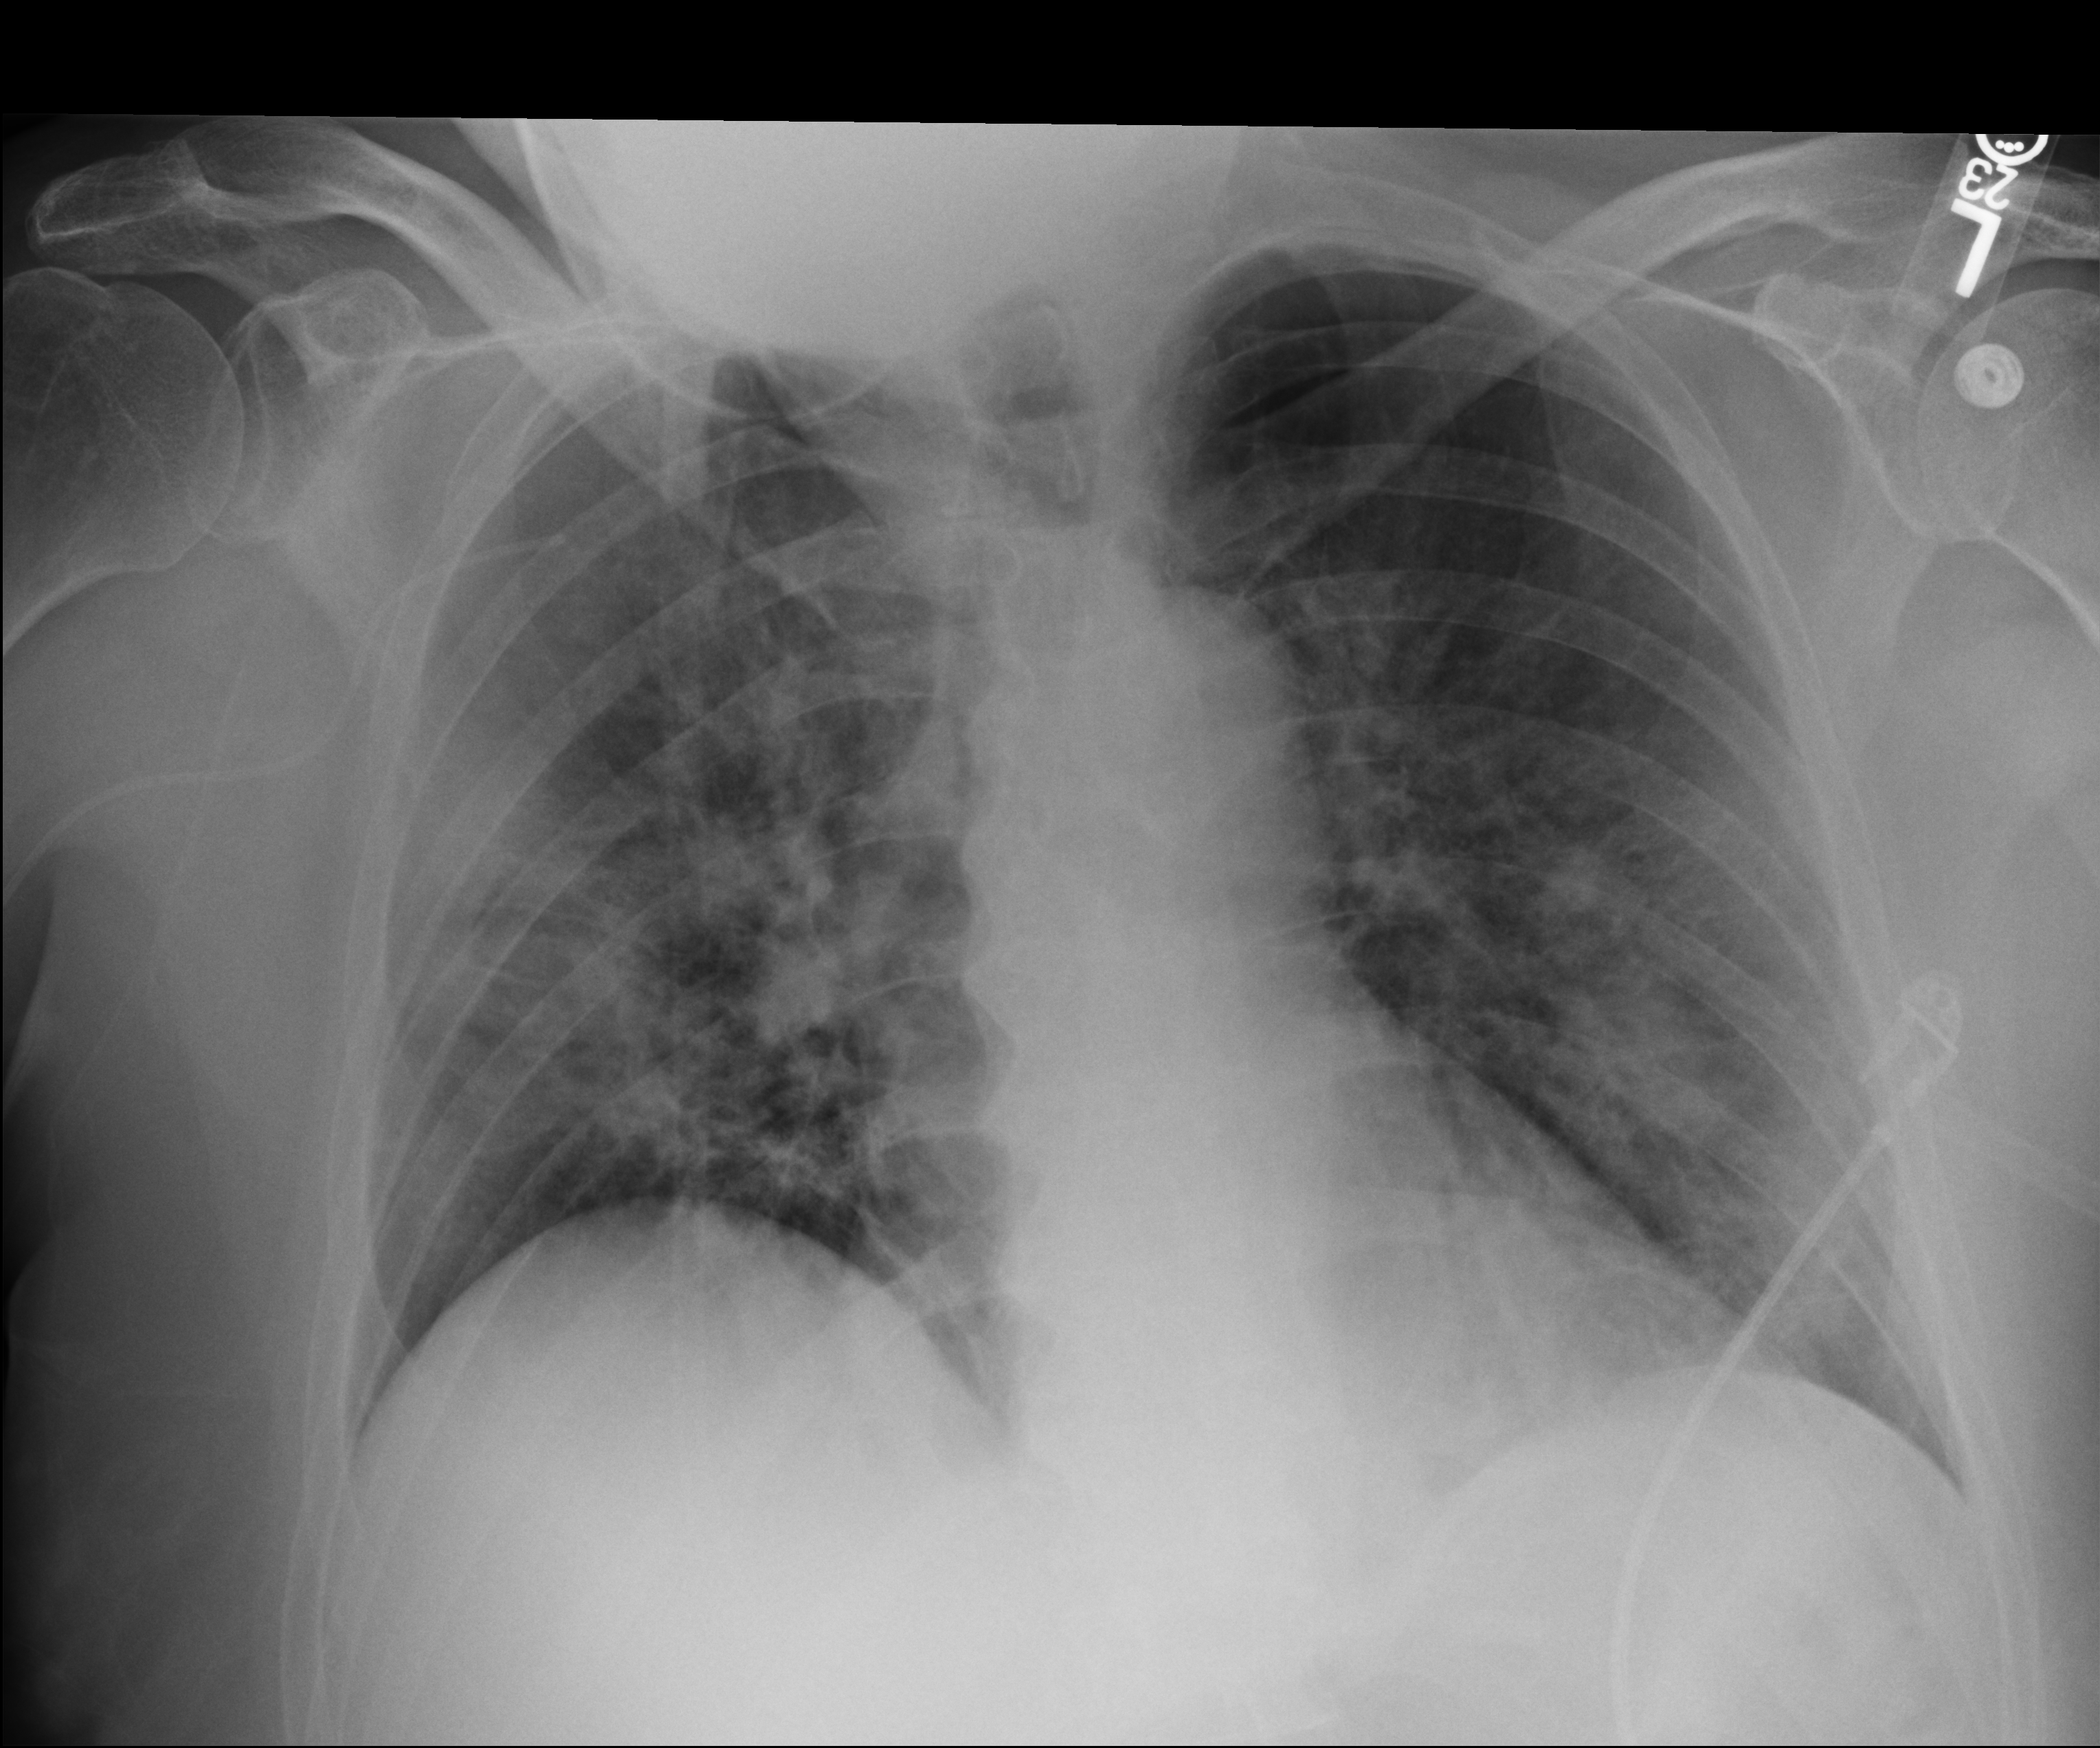
Bedside chest radiograph (computed radiography); anteroposterior (AP) projection. Patient hospitalised with COVID-19; male, aged 60–74 years.
Hospital-stay facts (about this admission, not read from this image; timing relative to this image not recorded):
- smoking status (admission record): never
- admitted to intensive care during this hospital stay: no